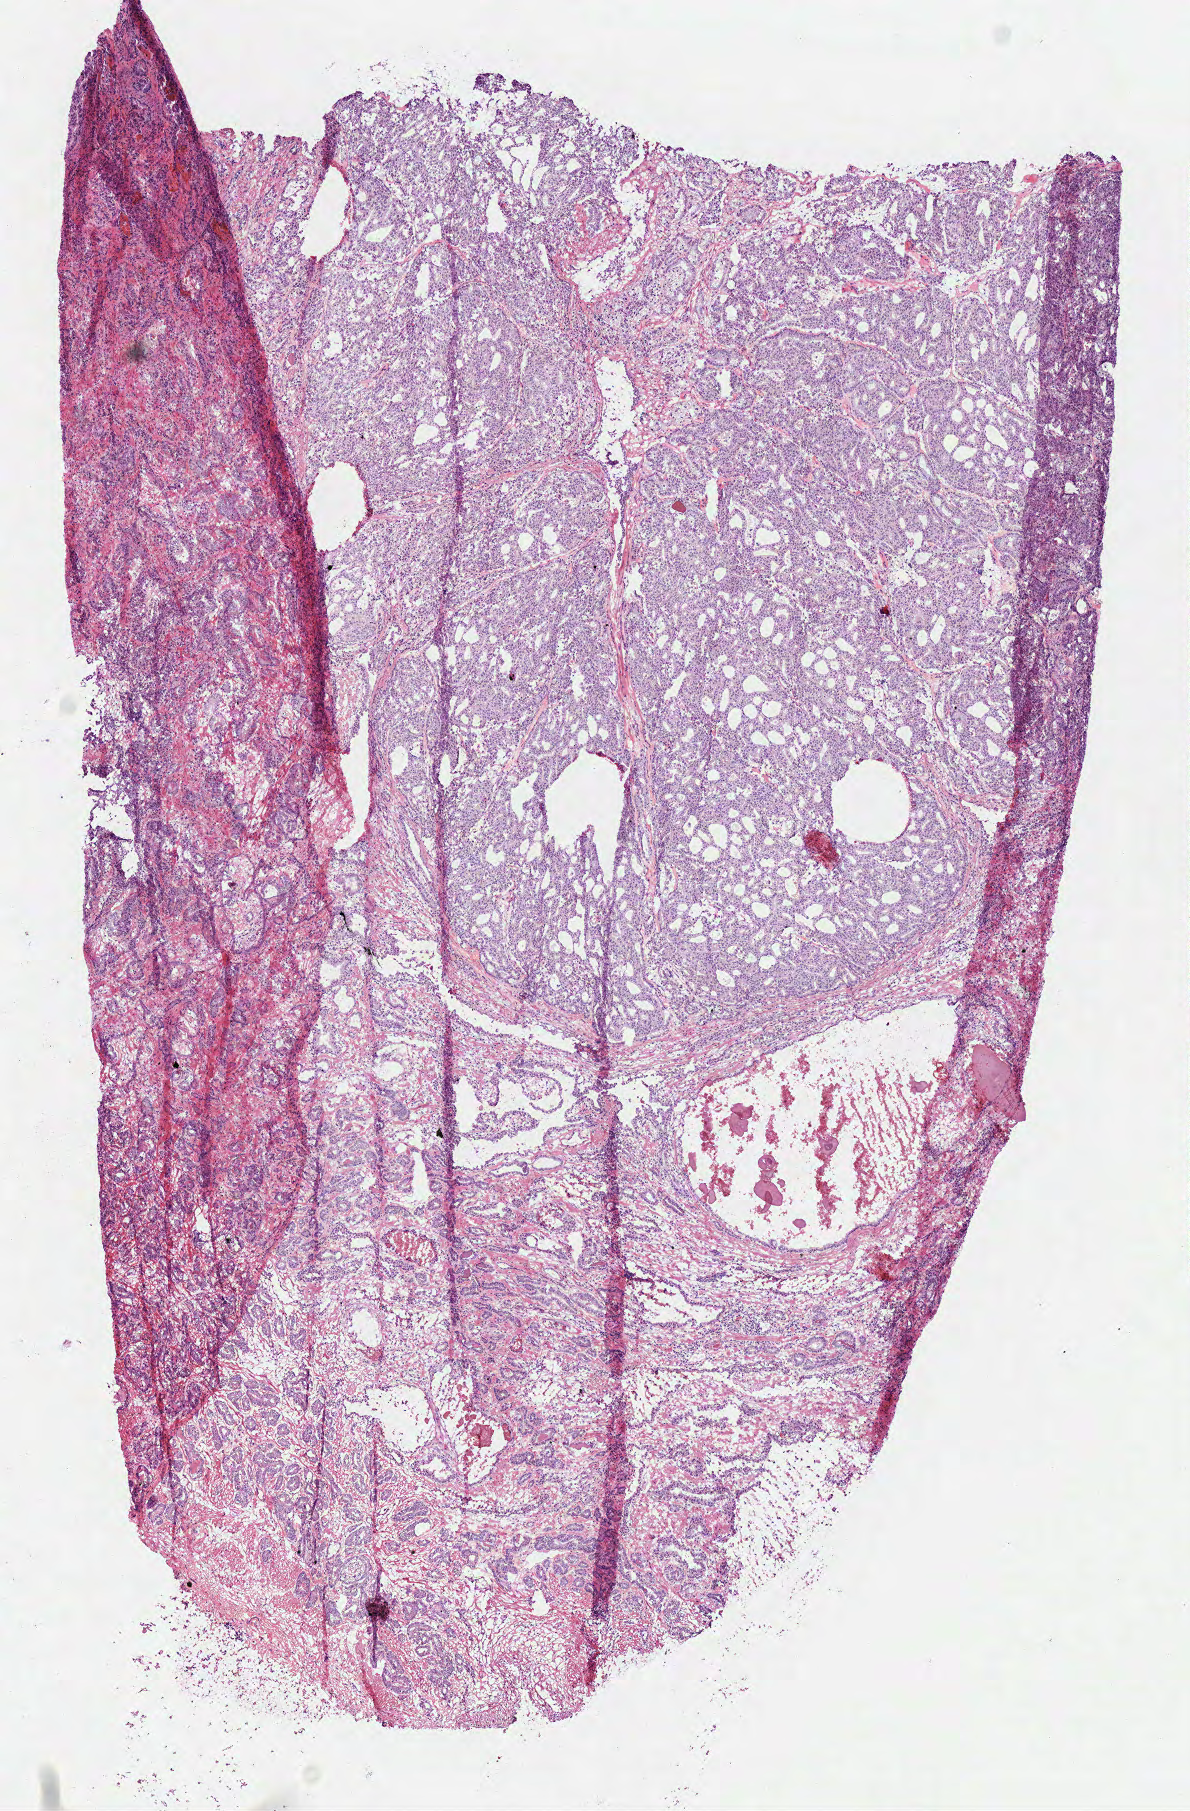
Digitized H&E tissue section (whole slide), low-resolution overview of the scanned area, about 4.7 x 7.1 mm (from a 40x scan). Frozen section from the top of the tissue portion. Sample: primary tumour, prostate. Male, age 62 years at initial diagnosis. Gleason score: 7 (3+4). Slide review estimates, as recorded: tumour cells 95%, tumour nuclei 95%, normal cells 0%, stromal cells 5%, necrosis 0%.
* histologic diagnosis: Acinar cell carcinoma (prostate gland)
* lymph nodes positive (case pathology): 0 of 10 examined